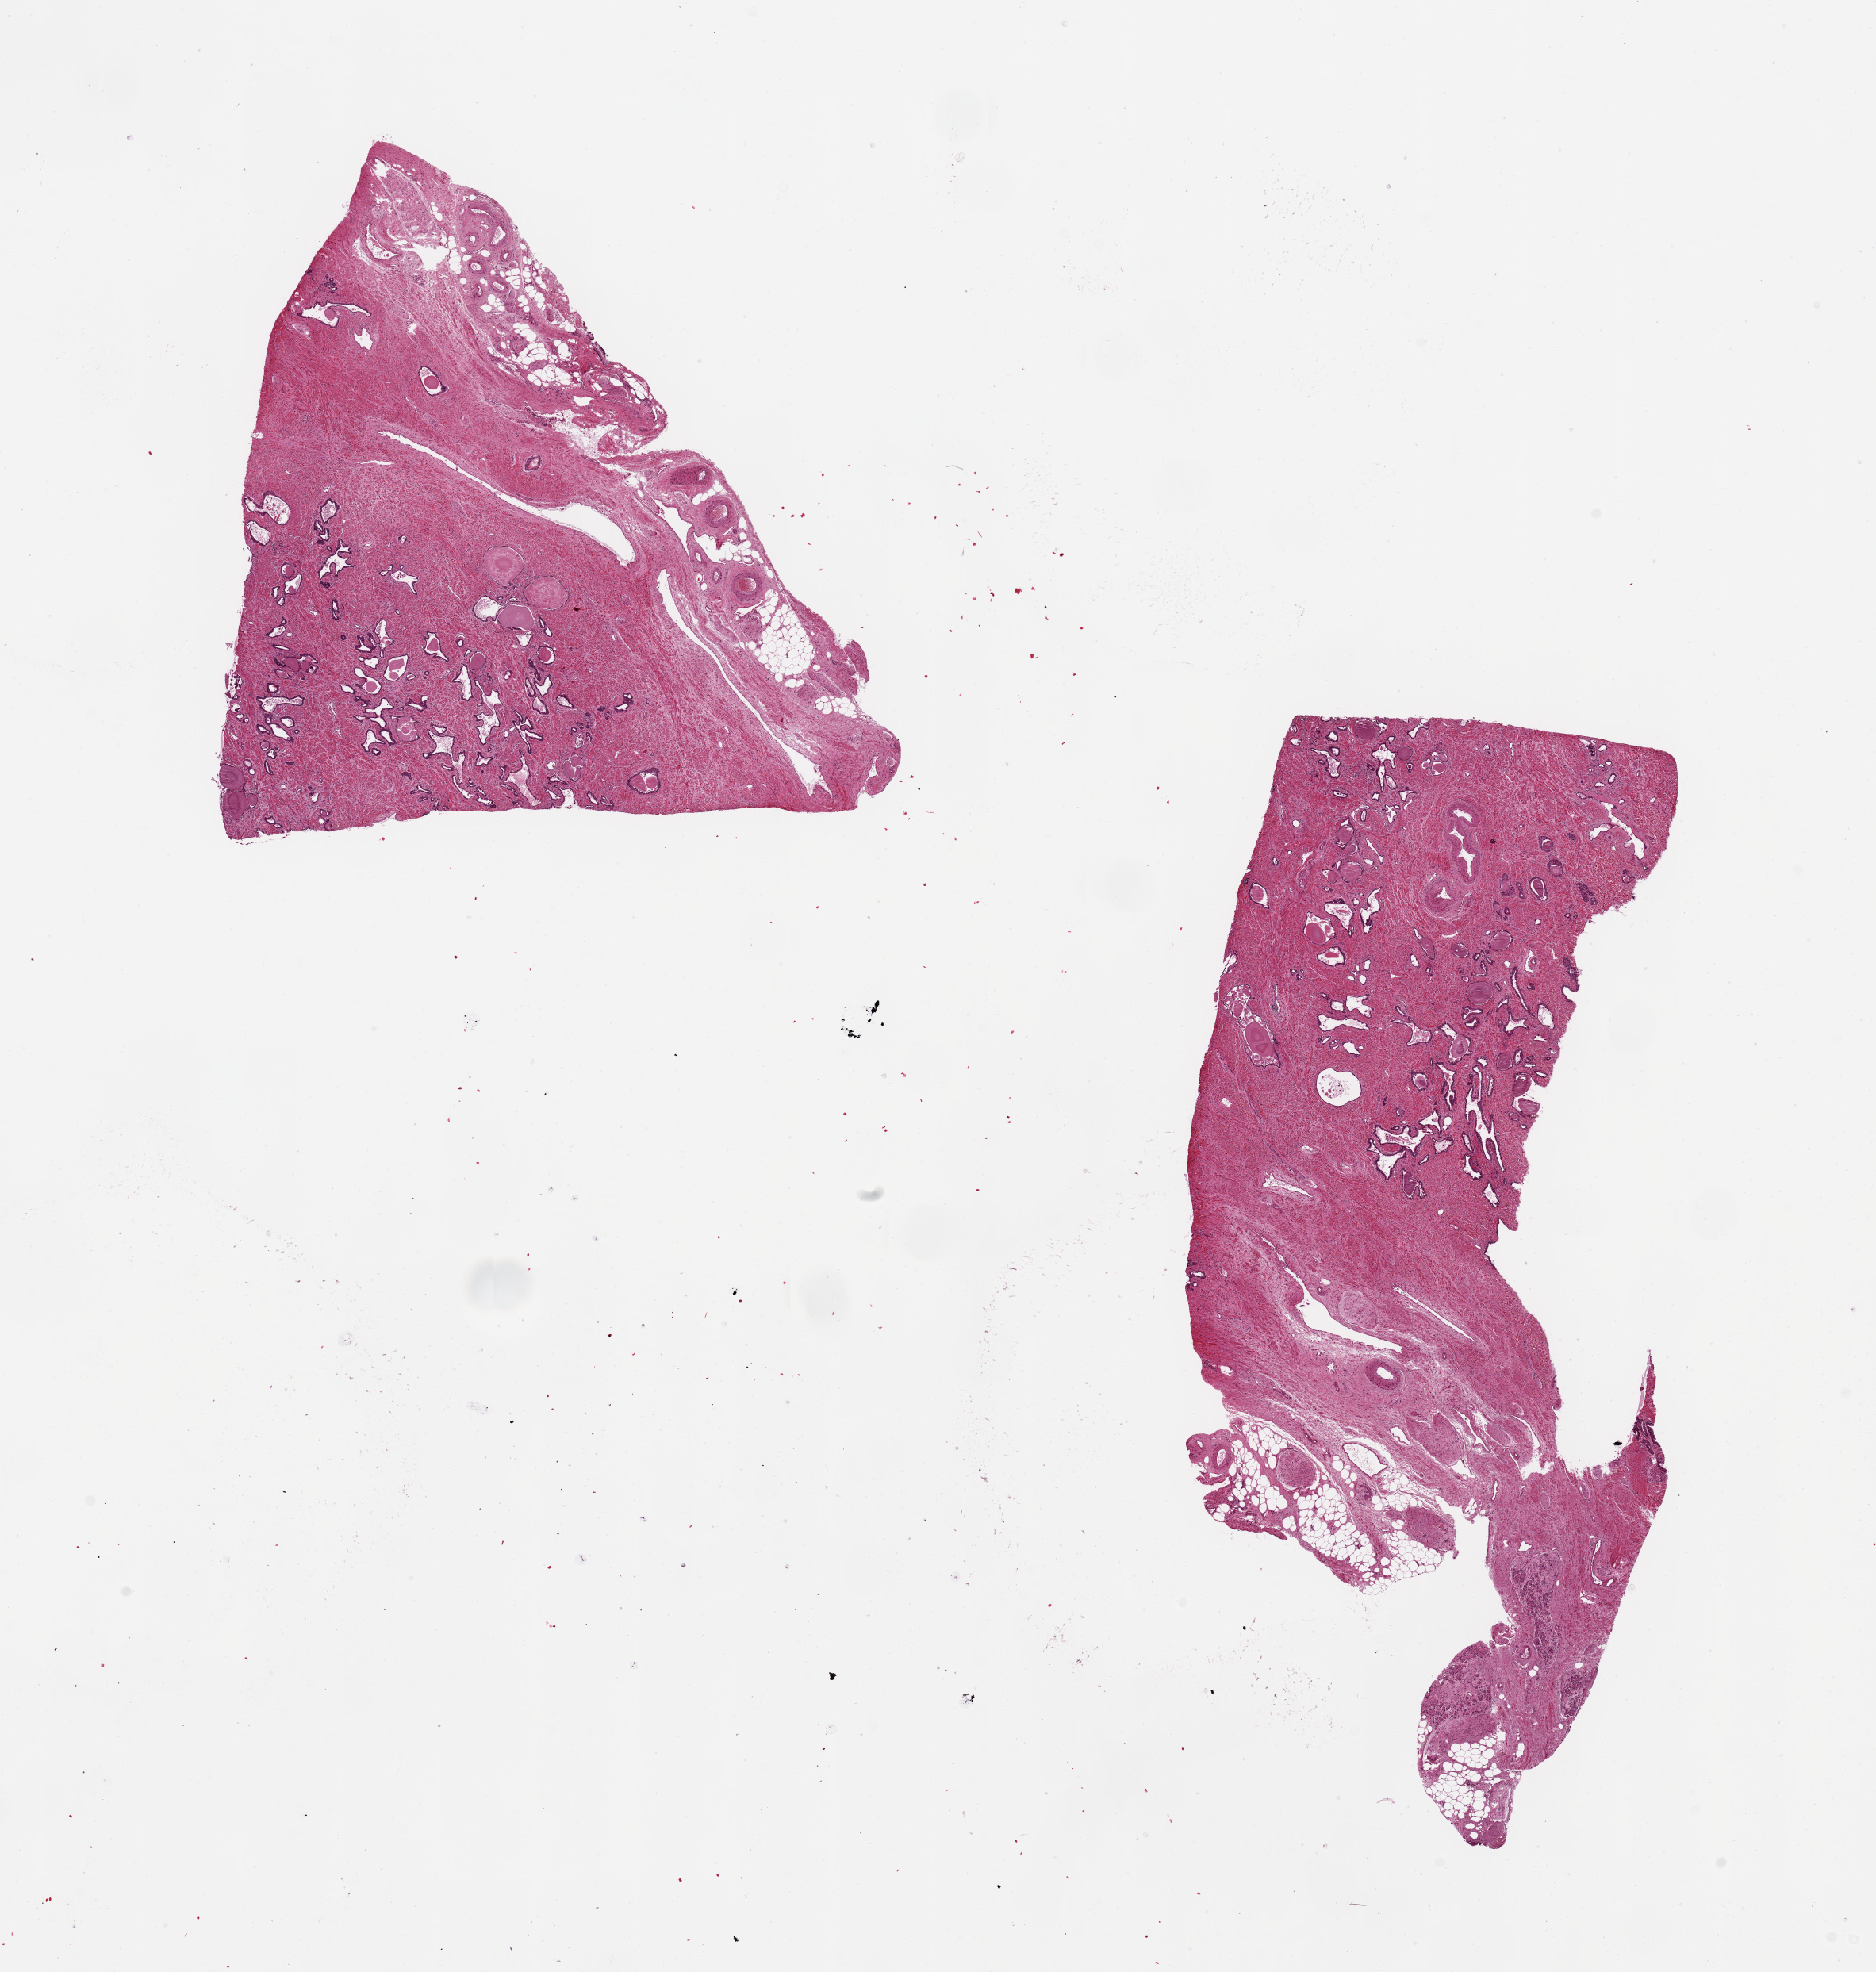
Whole-slide image, H&E stain — shown as a low-resolution overview of the whole scanned area (about 18.7 x 19.7 mm, slide scanned at 20x). PAXgene-fixed, paraffin-embedded tissue. Sampled site (target tissue): prostate. Donor tissue sample.
Pathologist's review note for this sample: 2 pieces. 7x7 & 11x5mm; well preserved glands; 1 piece with 2 mm focus of ganglion cells; 1 with 1mm external adipose.